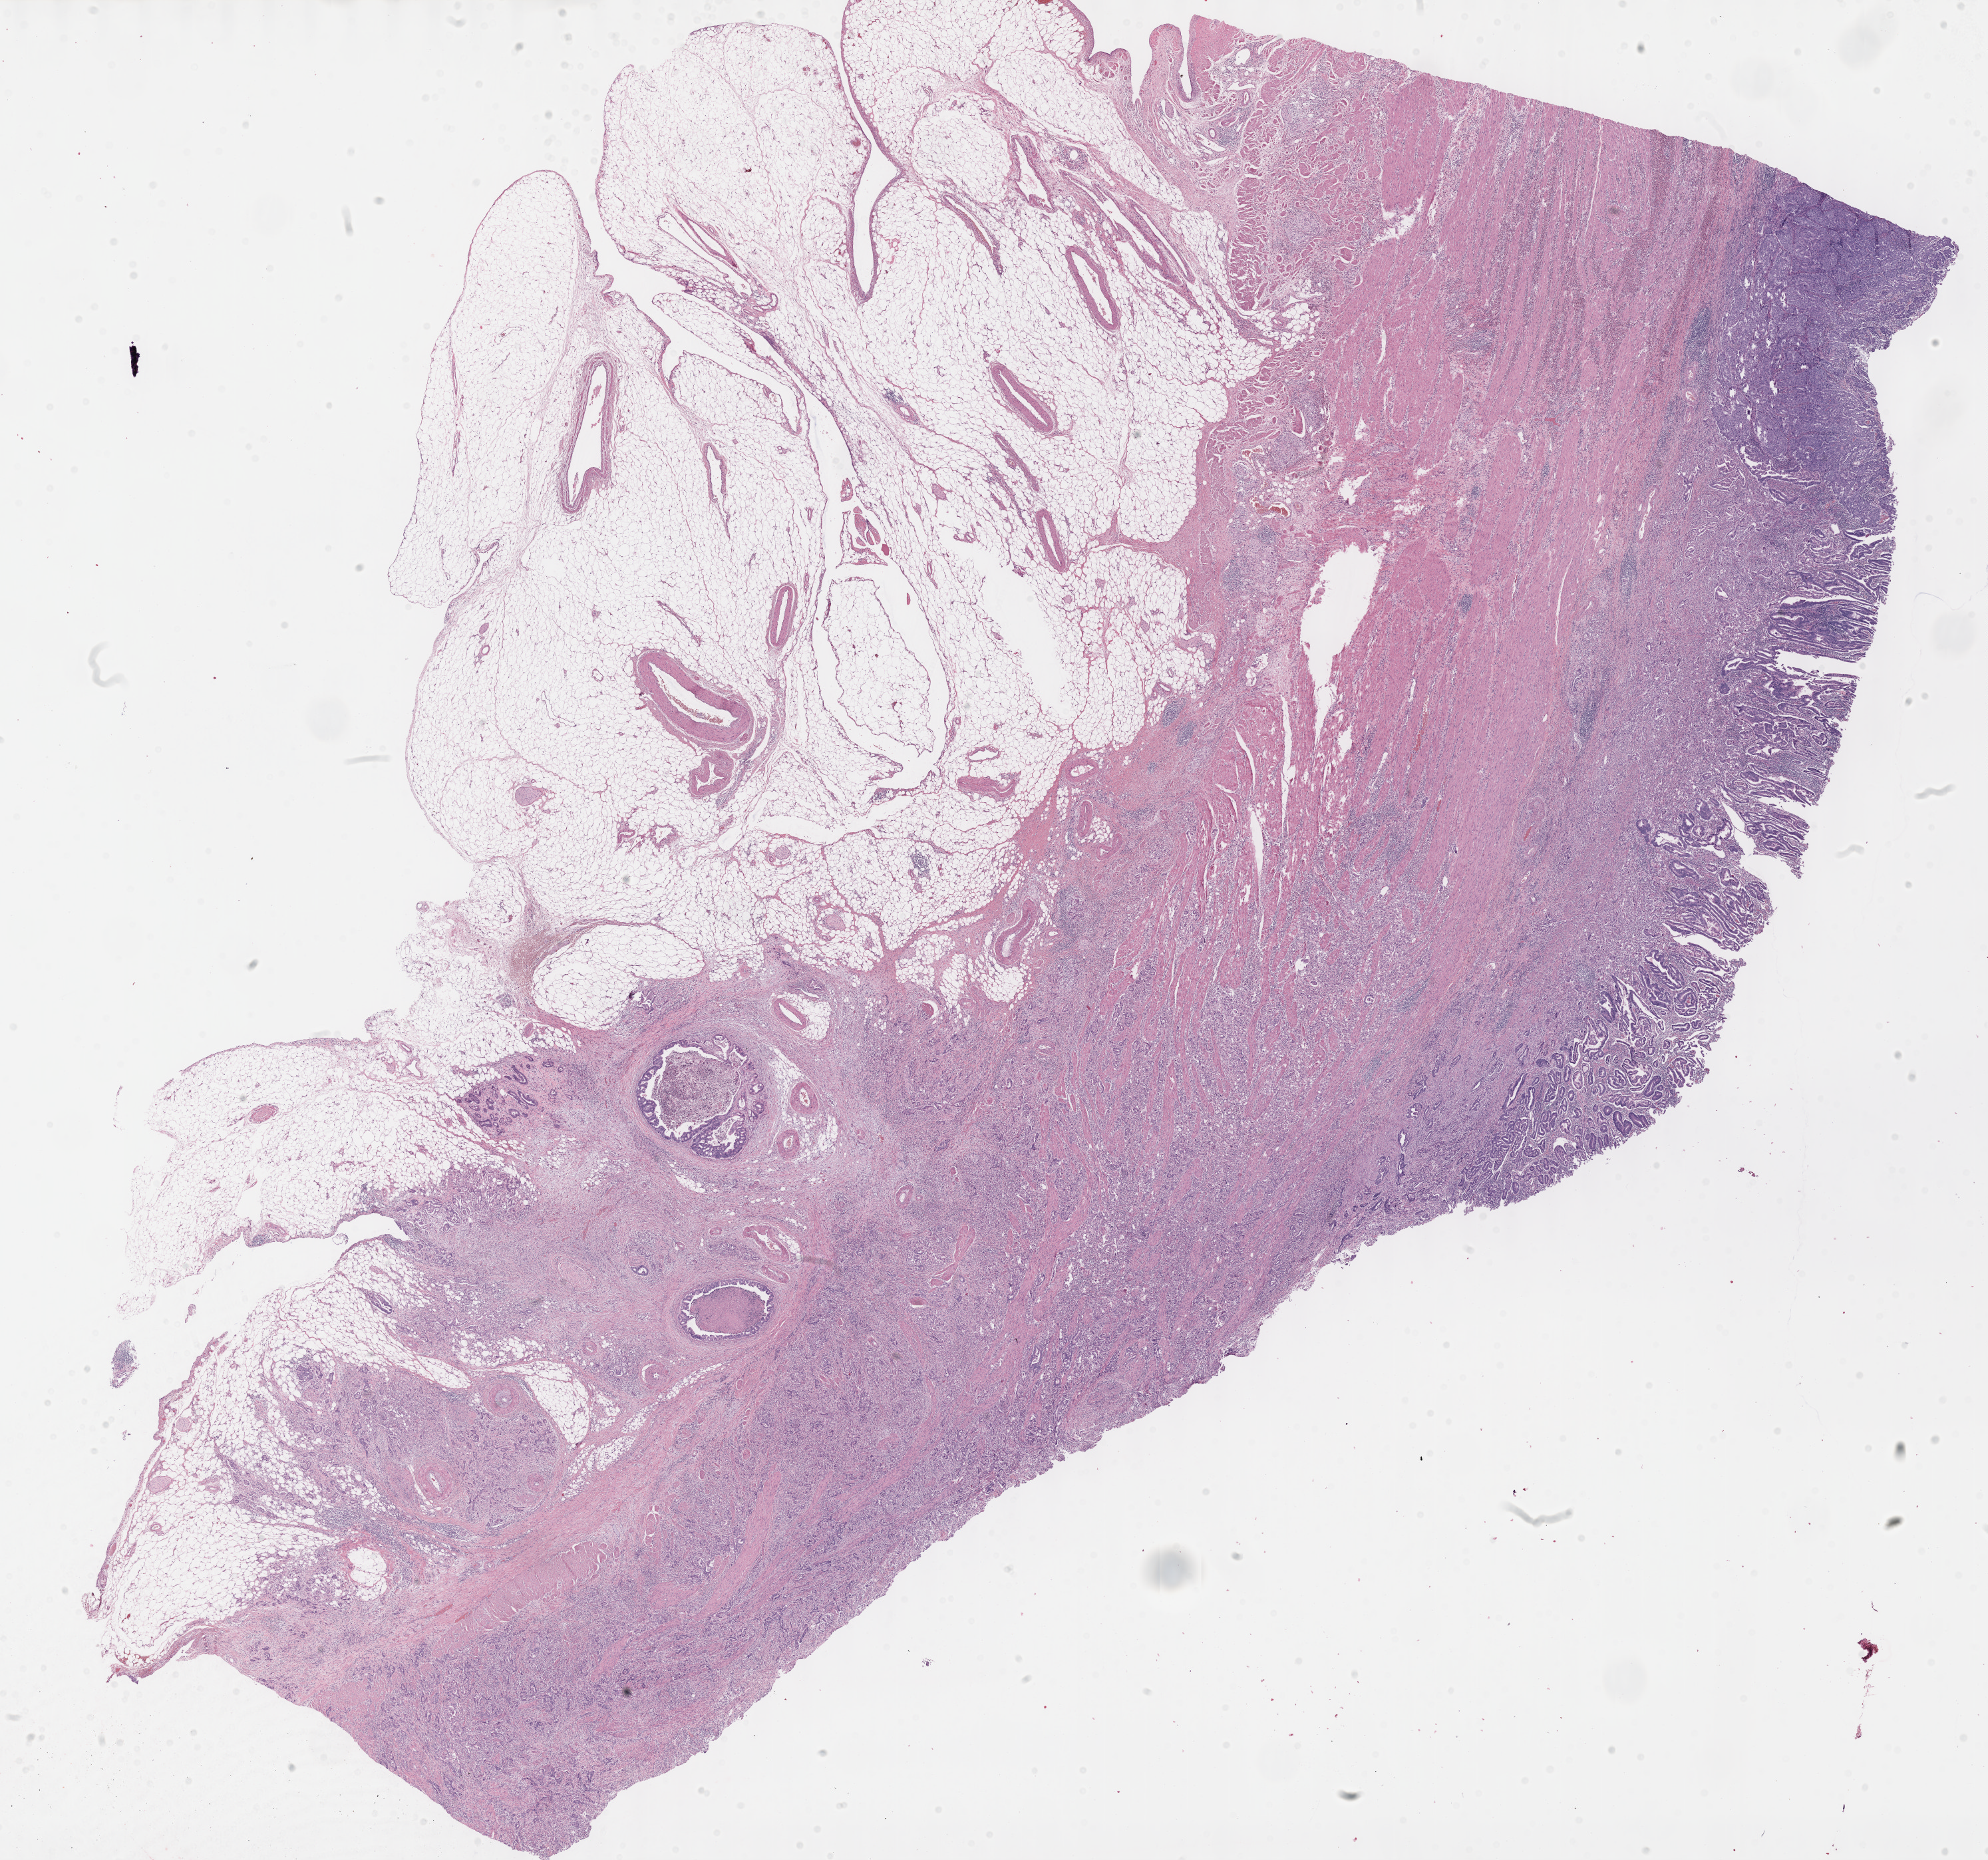
H&E whole-slide image, low-resolution overview of the scanned area, about 24.1 x 22.6 mm (acquisition: 40x scan); formalin-fixed paraffin-embedded (FFPE) diagnostic section; stomach, primary tumour sample. Male, age 68 years at initial diagnosis. Histologic grade: G3 (poorly differentiated).
Lymph nodes positive (case pathology): 6 of 23 examined. Diagnosis: Adenocarcinoma, intestinal type. AJCC pathologic stage: IIIA (7th edition). TNM: T3 N2 M0.